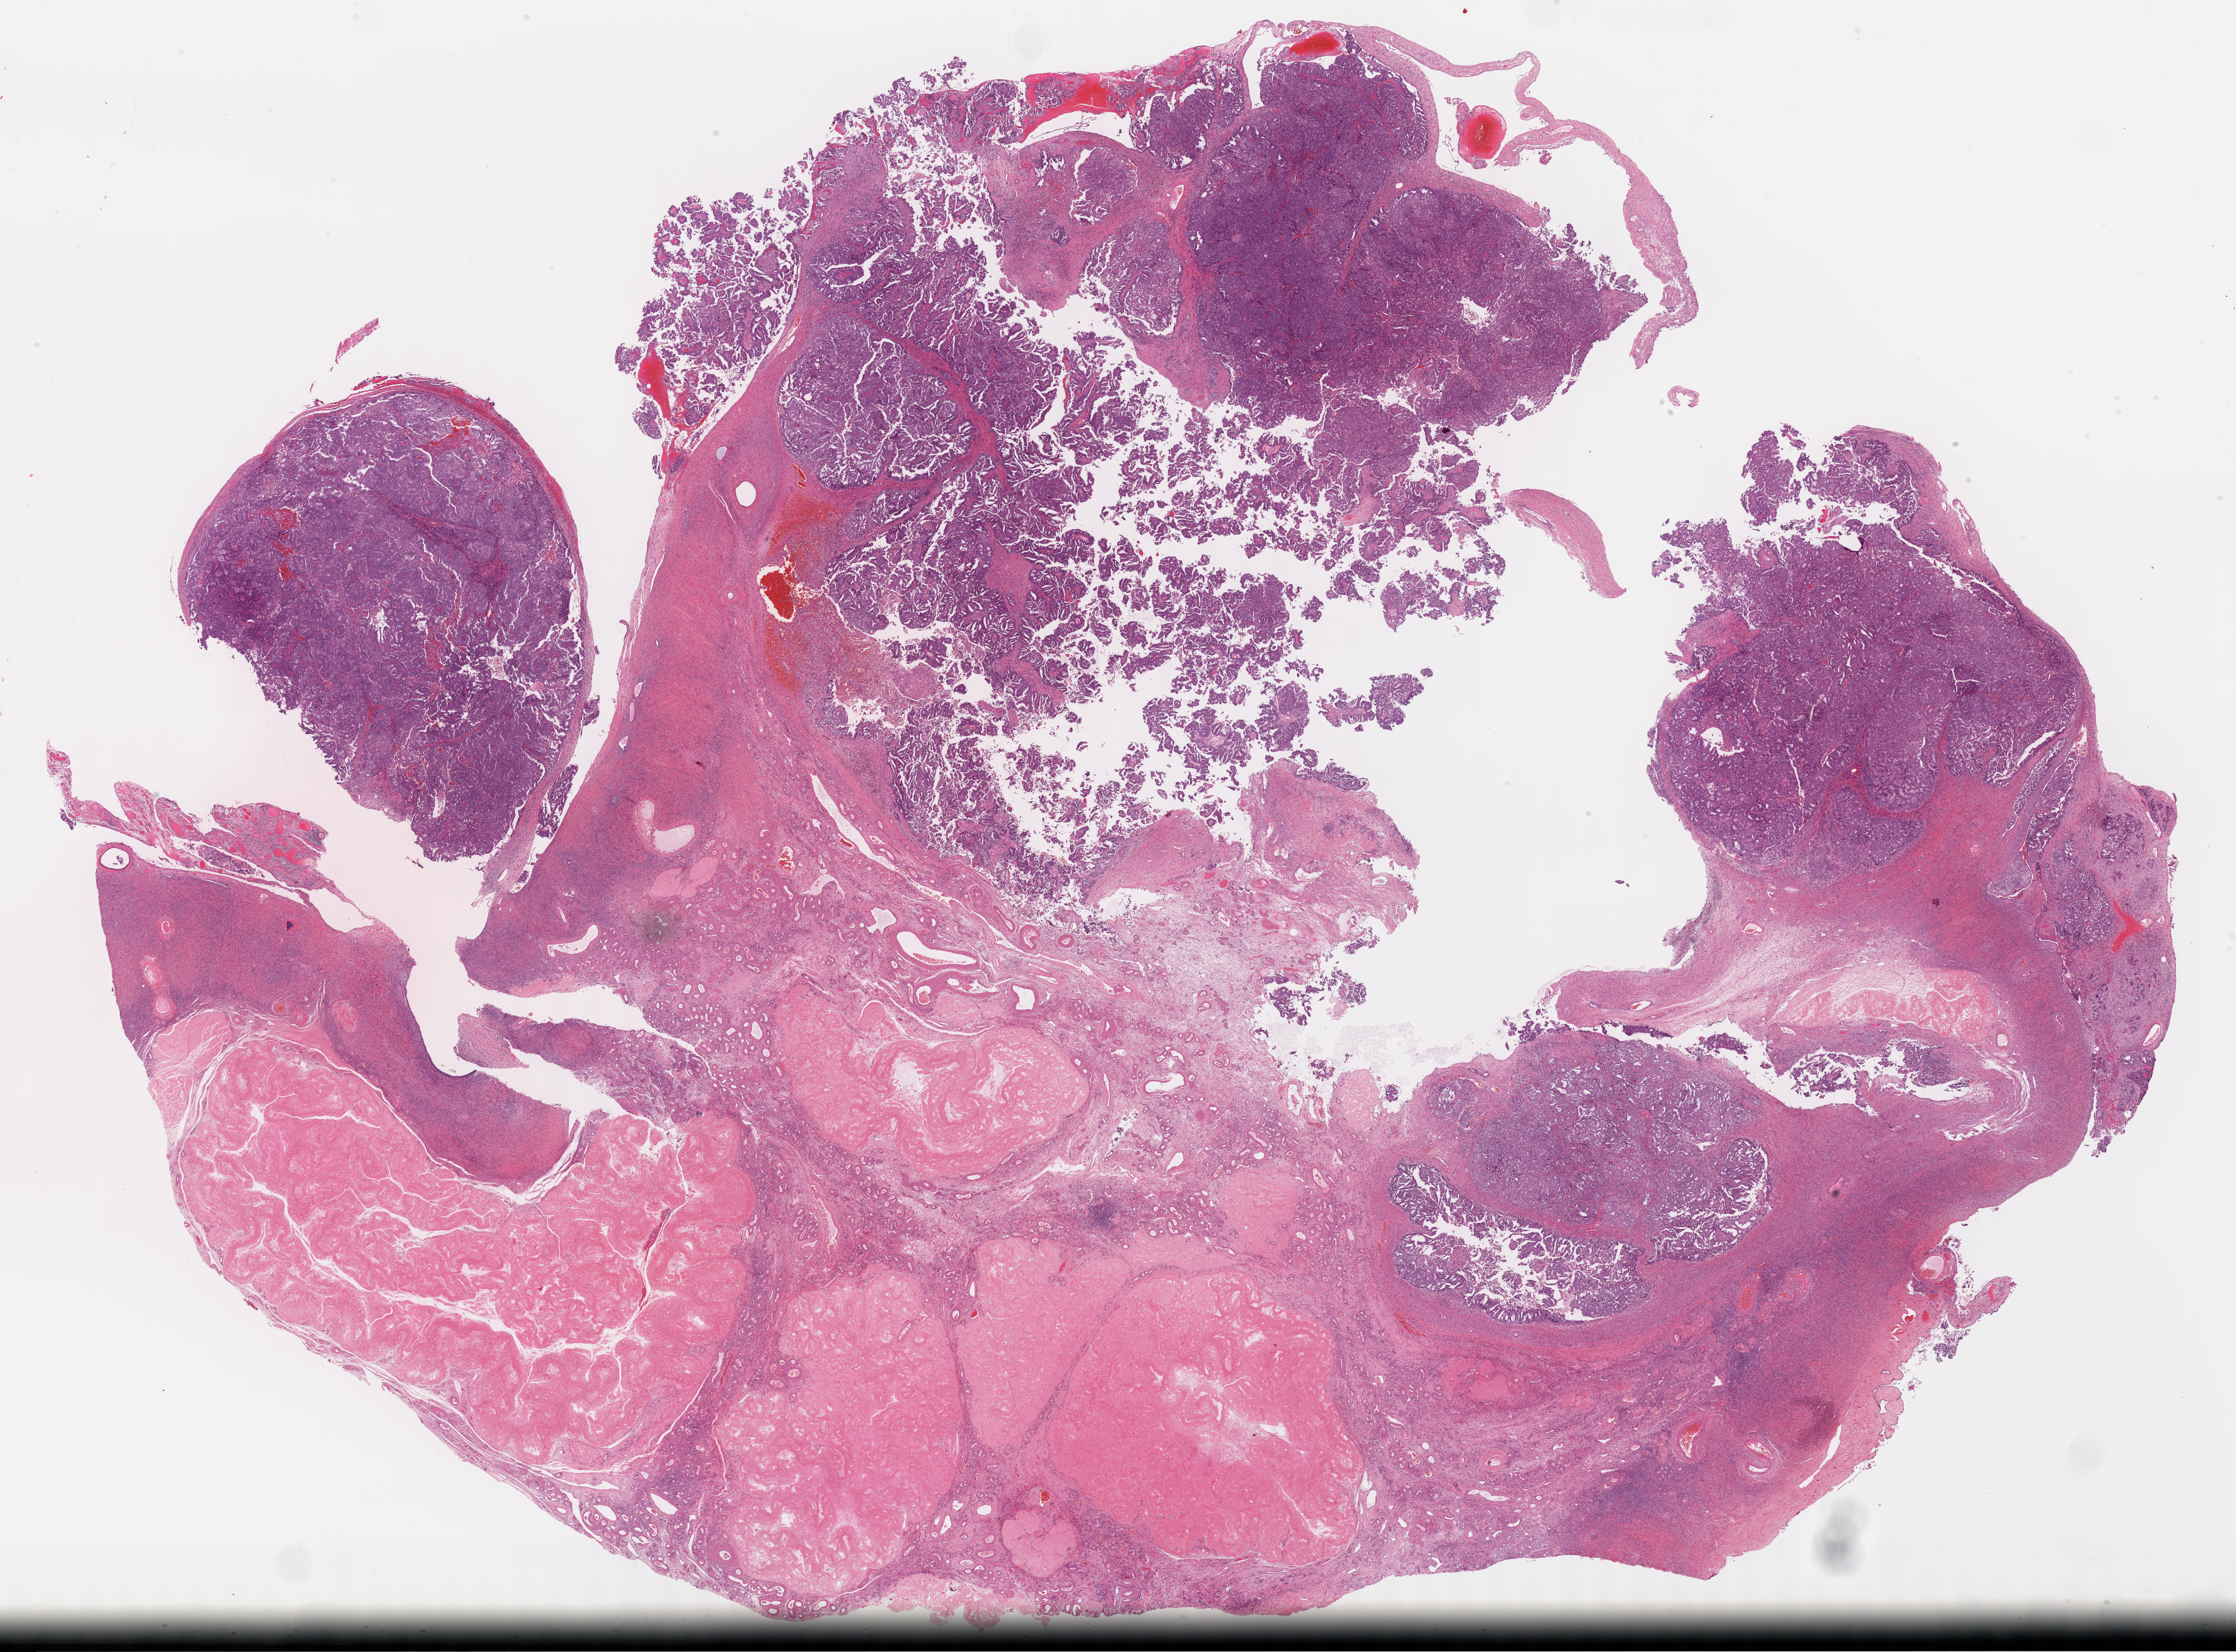
H&E-stained whole-slide image — a low-resolution overview of the entire scanned area, about 31.2 x 23.1 mm (slide scanned at 40x); formalin-fixed paraffin-embedded (FFPE) diagnostic section; primary tumour sample from the ovary. Female, age 59 years at initial diagnosis. Histologic grade: G3 (poorly differentiated).
• FIGO stage: IV
• laterality: left
• pathologic diagnosis: Serous cystadenocarcinoma, NOS